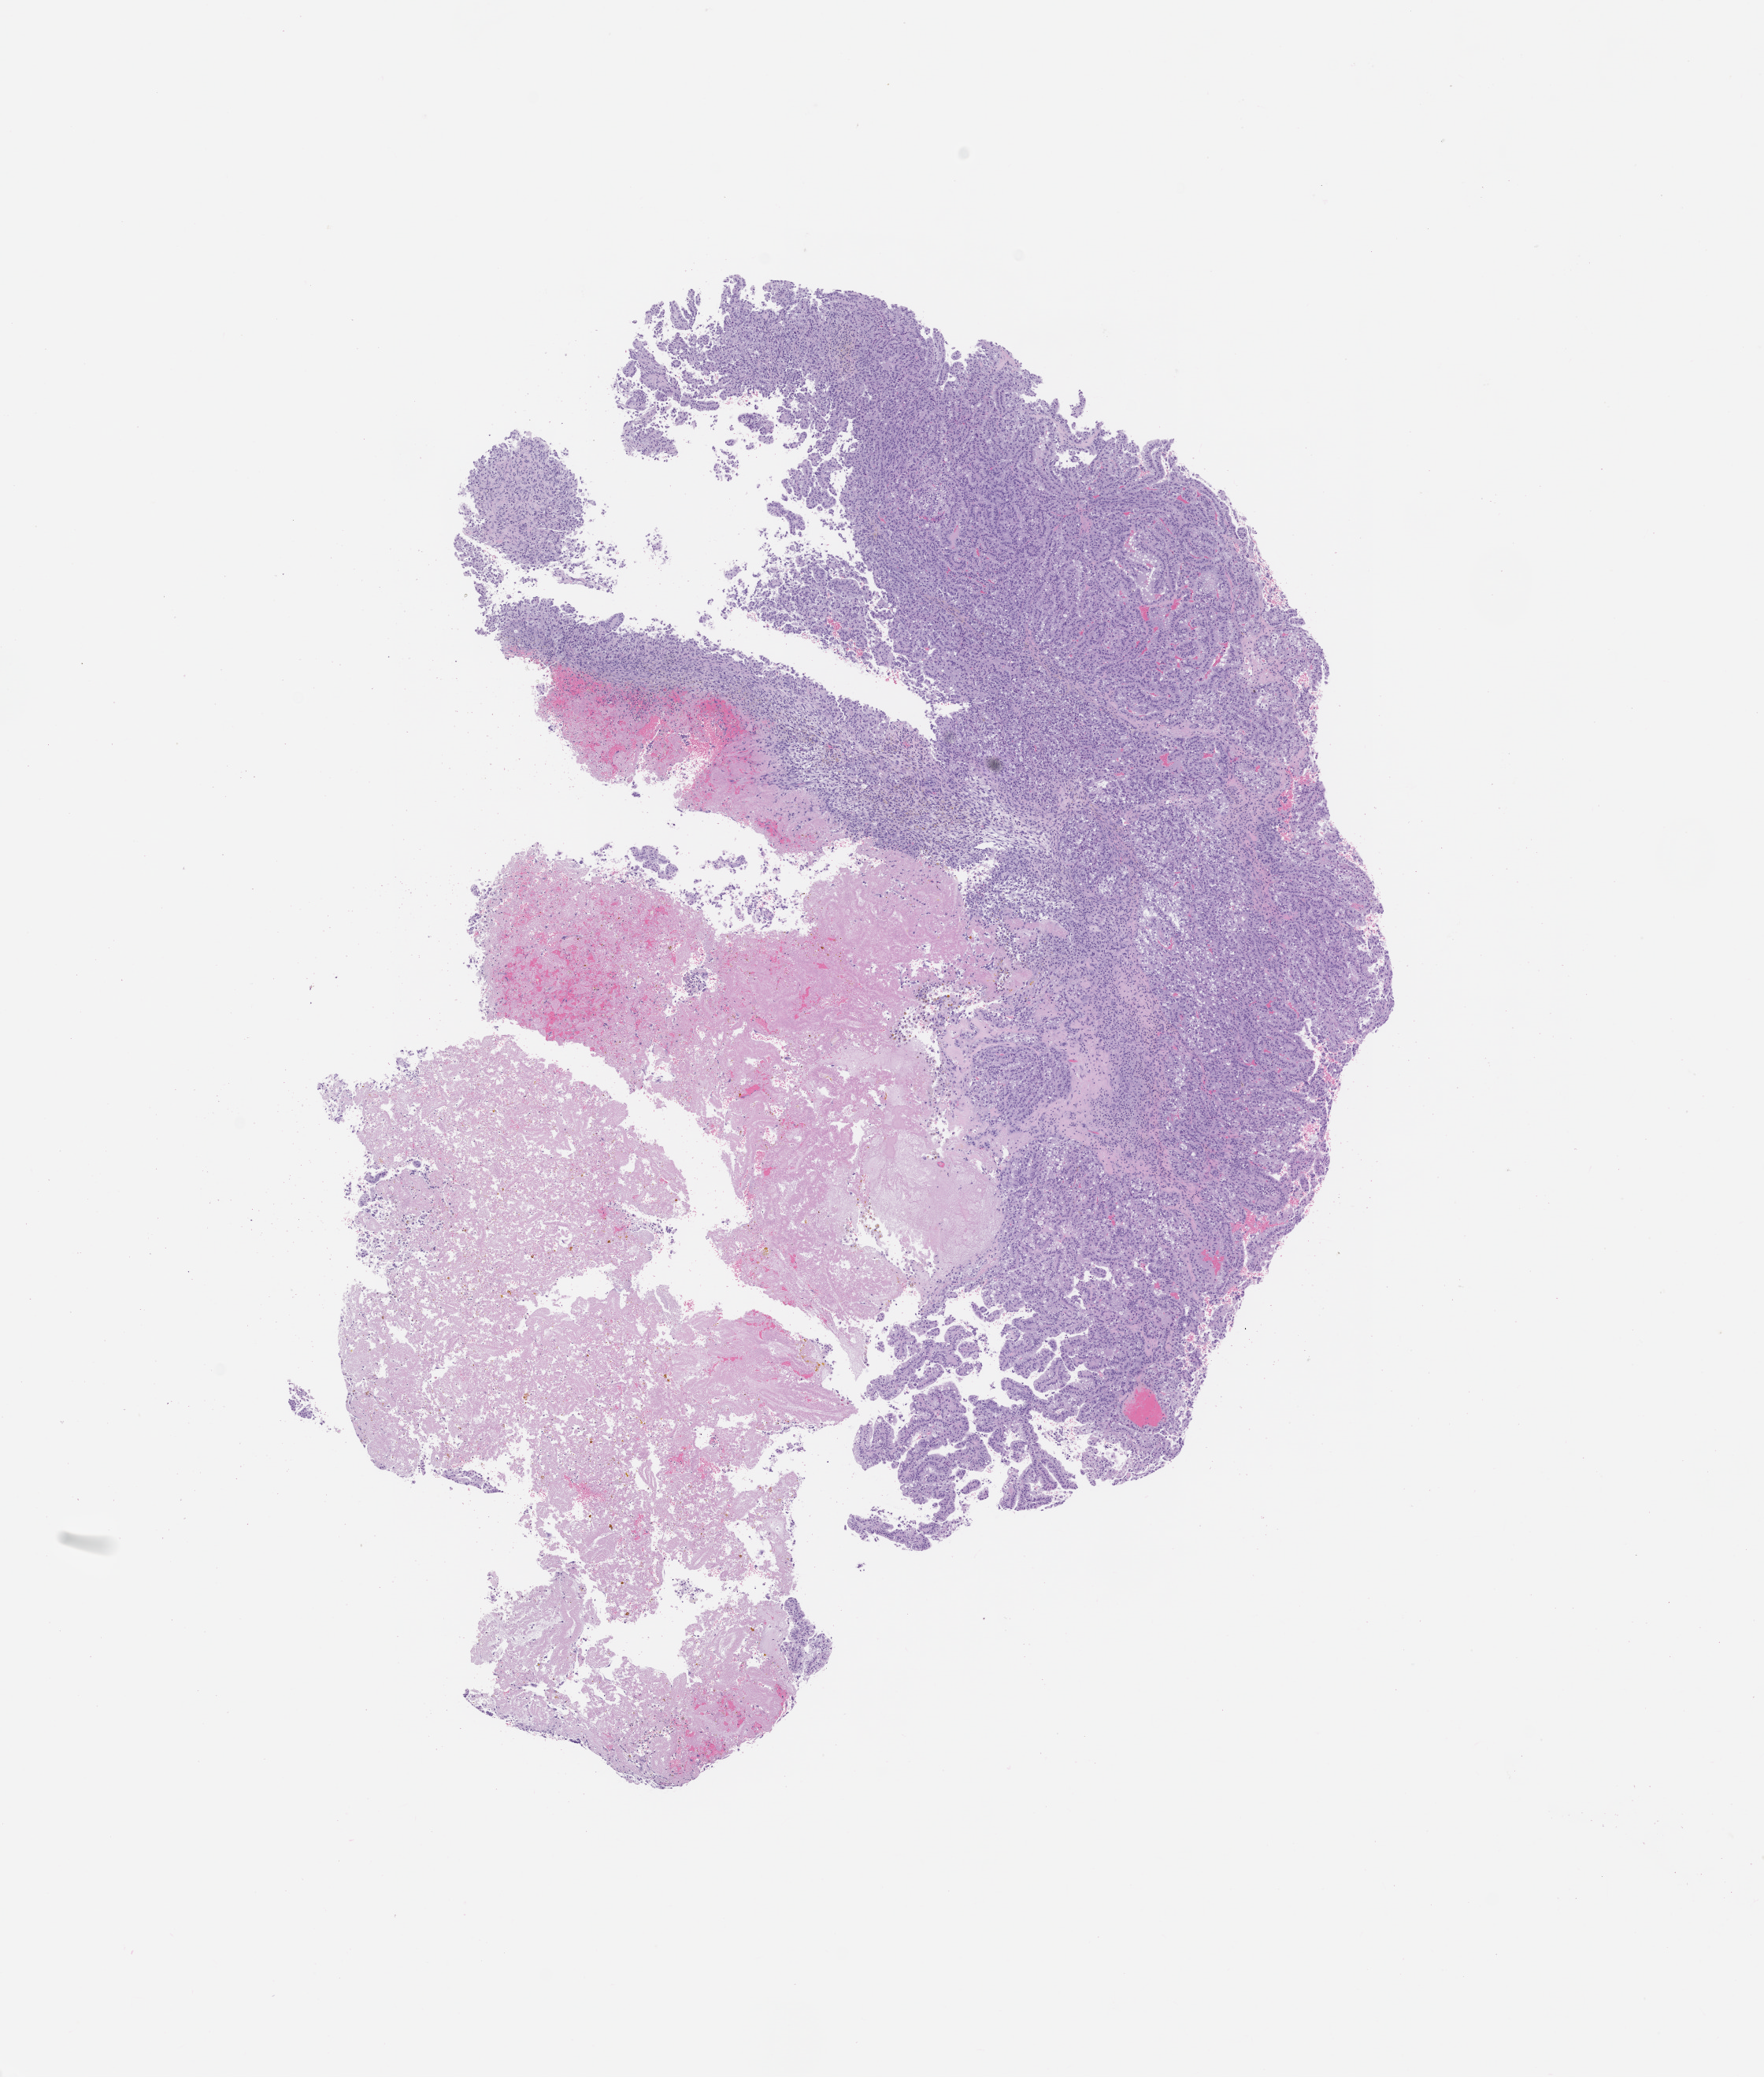
Hematoxylin and eosin (H&E) whole-slide image of a patient-derived xenograft (PDX) tumor grown in a mouse, passage 1 — shown as a low-resolution overview of the whole scanned area (about 9.0 x 10.6 mm); formalin-fixed paraffin-embedded section; tumor site category: genitourinary tract.
Originating patient diagnosis: Renal Cell Carcinoma, Not Otherwise Specified.